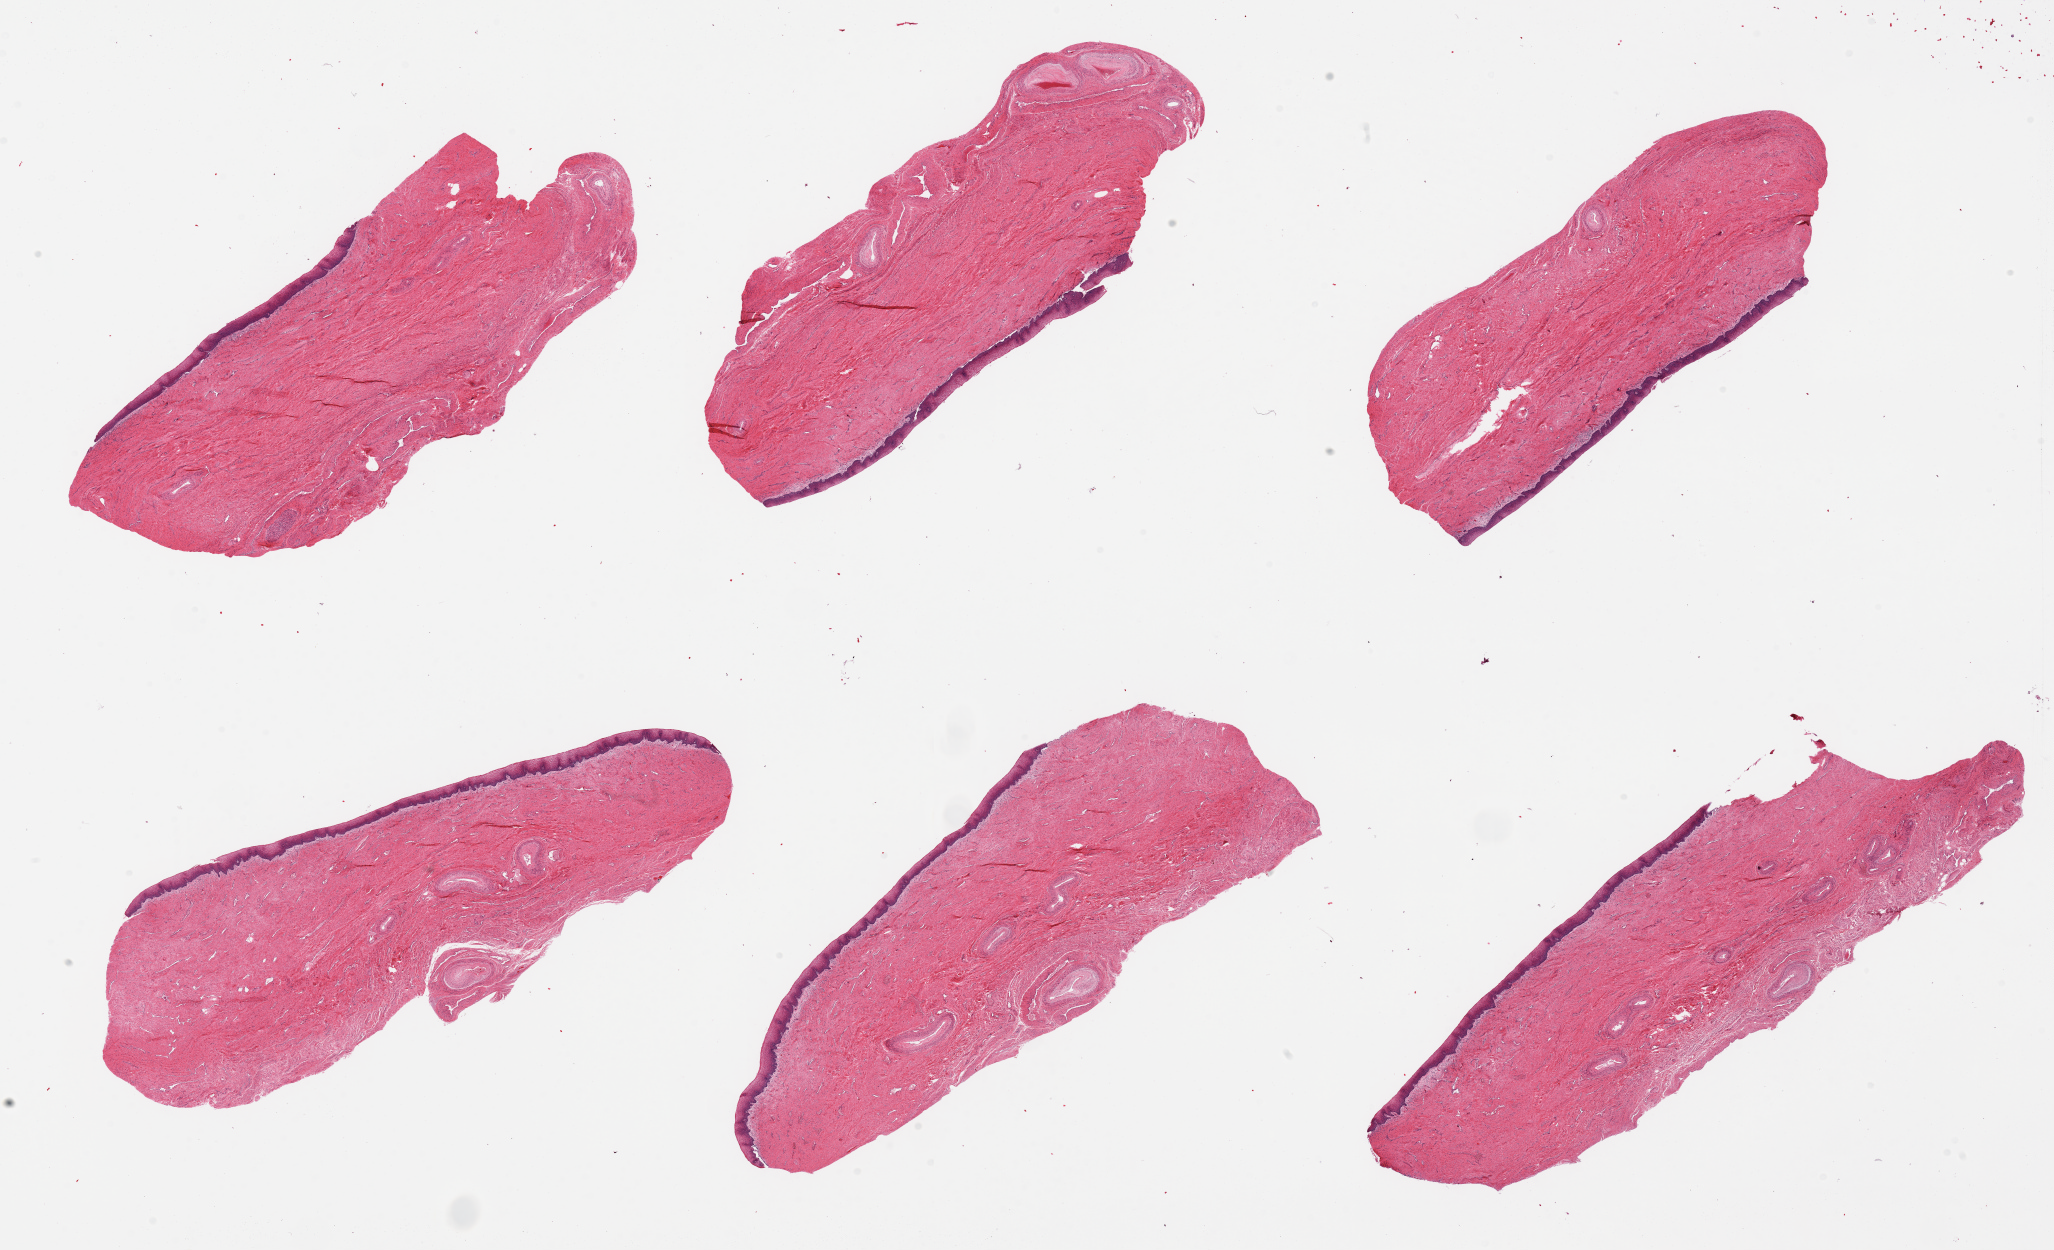
Digitized H&E-stained section, whole scanned area (about 32.5 x 19.8 mm) shown as a low-resolution overview. PAXgene-fixed, paraffin-embedded tissue. Sampled site (target tissue): vagina. Tissue donor sample.
- reviewer comment on this tissue sample: 6 pieces, vascular thickening